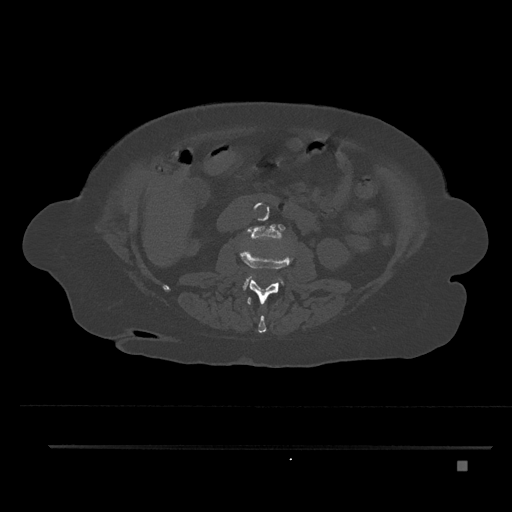
CT including the spine, one axial slice. Slice 168 of 797 in the series (ordered by position). Reconstruction kernel Br40s/3. 120 kVp. Bone window (W 1800 / L 400 HU). 0.5 mm slice thickness. 512 × 512 image matrix, field of view 437 × 437 mm. Female patient, age 76 years. From the clinical record (not read from this slice): primary cancer: lung.
Outlined on this slice (semi-automatically segmented with operator editing):
- L1 vertebra: bounding box [x1, y1, x2, y2] px = [247, 297, 278, 333]
- L2 vertebra: [240, 251, 293, 305]
- L3 vertebra: [243, 224, 290, 288]